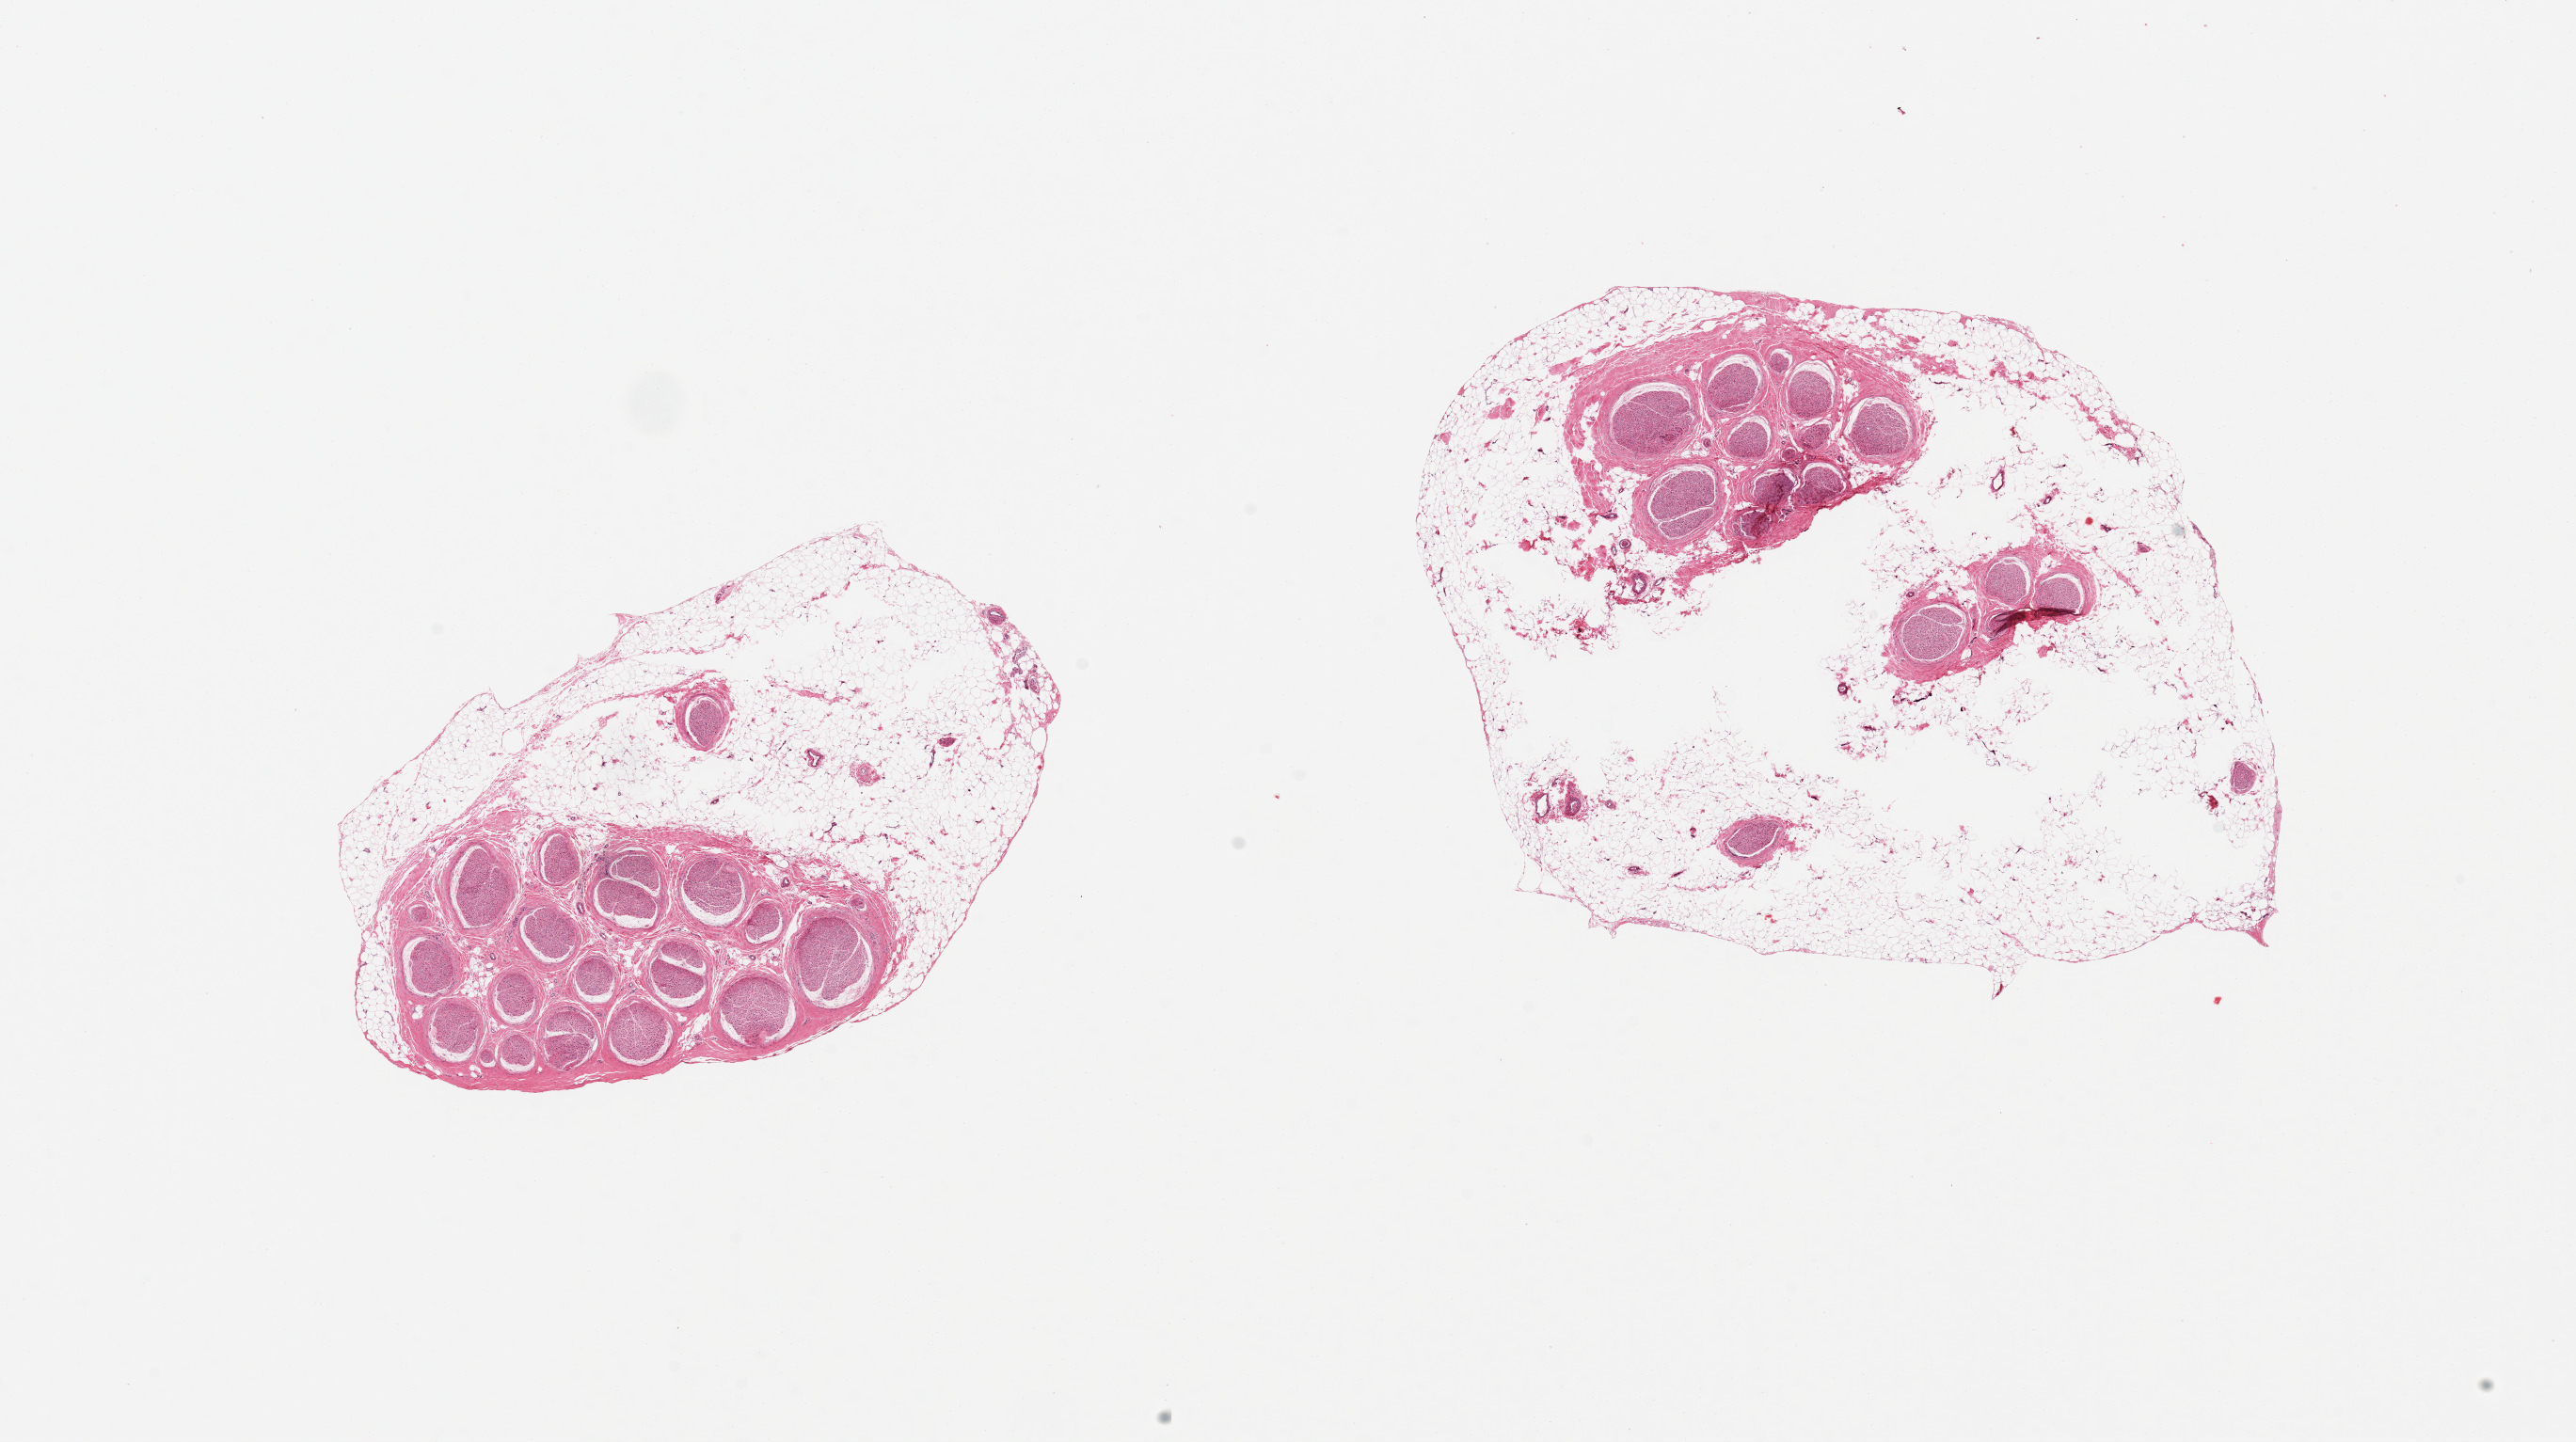
Haematoxylin and eosin whole-slide image, brightfield, whole scanned area (about 21.7 x 12.1 mm) shown as a low-resolution overview; PAXgene-fixed paraffin-embedded (PFPE) section; sampled site (target tissue): tibial nerve; donor tissue sample. Donor: male.
• review note (as recorded): 2 pieces, 6x3.3 & 6.2x 6.3mm; > 50% surrounding adipose